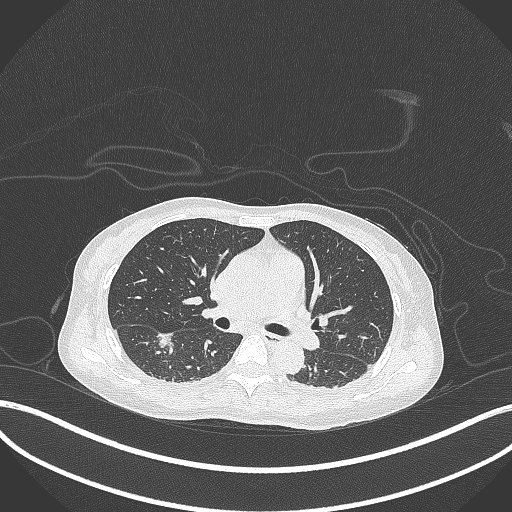
Chest CT, one axial slice; slice 181 of 261 in the series (ordered by position); 120 kVp; lung window (W 1500 / L -600 HU); 1 mm slice thickness; 512 × 512 image matrix, field of view 400 × 400 mm. Patient: female, 44 years. From the clinical record (not read from this slice): clinical TNM (as recorded): T1c N0 M0.
Annotated regions visible in this slice (bounding box drawn by a radiologist):
- lung tumour (recorded histology: adenocarcinoma): box from (x=155, y=330) to (x=176, y=353) px